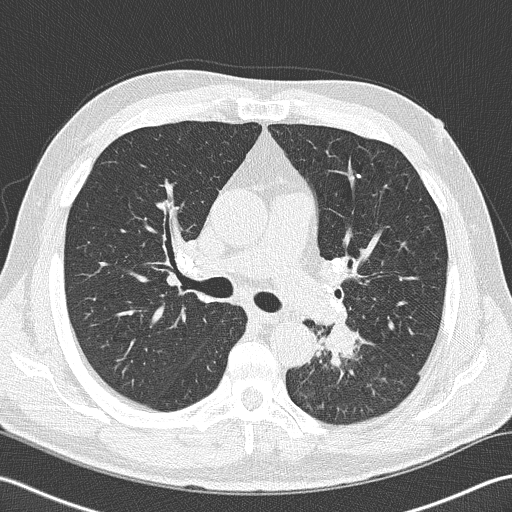
Low-dose screening chest CT, axial slice; second annual screen; lung window (W 1500 / L -600 HU); lung (sharp) reconstruction kernel (B50f). Male participant, aged 57 years at enrolment. Former smoker at enrolment.
Lesion marked by an expert reader, box from (x=294, y=311) to (x=374, y=385) px. Screening reader's record for this exam (one nodule recorded; not confirmed to be the boxed lesion): non-calcified nodule or mass ≥4 mm, left lower lobe, 40 × 30 mm, spiculated (stellate) margins, soft tissue attenuation, pre-existing on the prior screen: no.